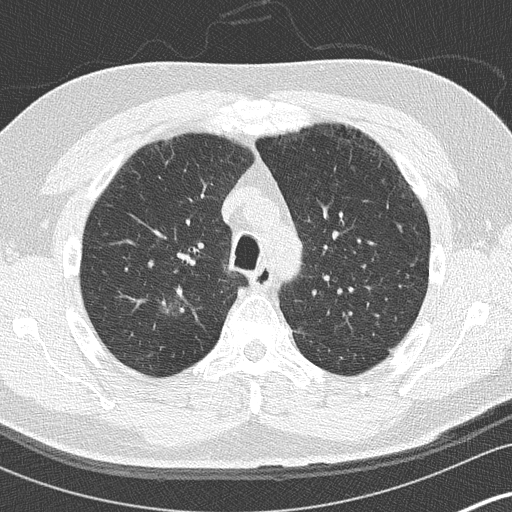
Low-dose screening chest CT, axial slice. First (baseline) screen. Lung window (W 1500 / L -600 HU). 2 mm slice thickness. 120 kVp. 512 × 512 image matrix. Male, age 59 years at enrolment.
Expert-annotated lung lesion, box from (x=148, y=287) to (x=204, y=343) px. The exam's reader record, not a measurement of the box and not confirmed to be the same lesion: non-calcified nodule or mass ≥4 mm, right upper lobe, 16 × 16 mm, ground glass attenuation. Official screen result: positive, change unspecified: nodule(s) >= 4 mm or enlarging nodule(s), mass(es), or other non-specific abnormalities suspicious for lung cancer. Participant outcome: lung cancer diagnosed 456 days after this screen — bronchiolo-alveolar adenocarcinoma, NOS, right lower lobe, stage IA (AJCC 6th edition), 15 mm at pathology.